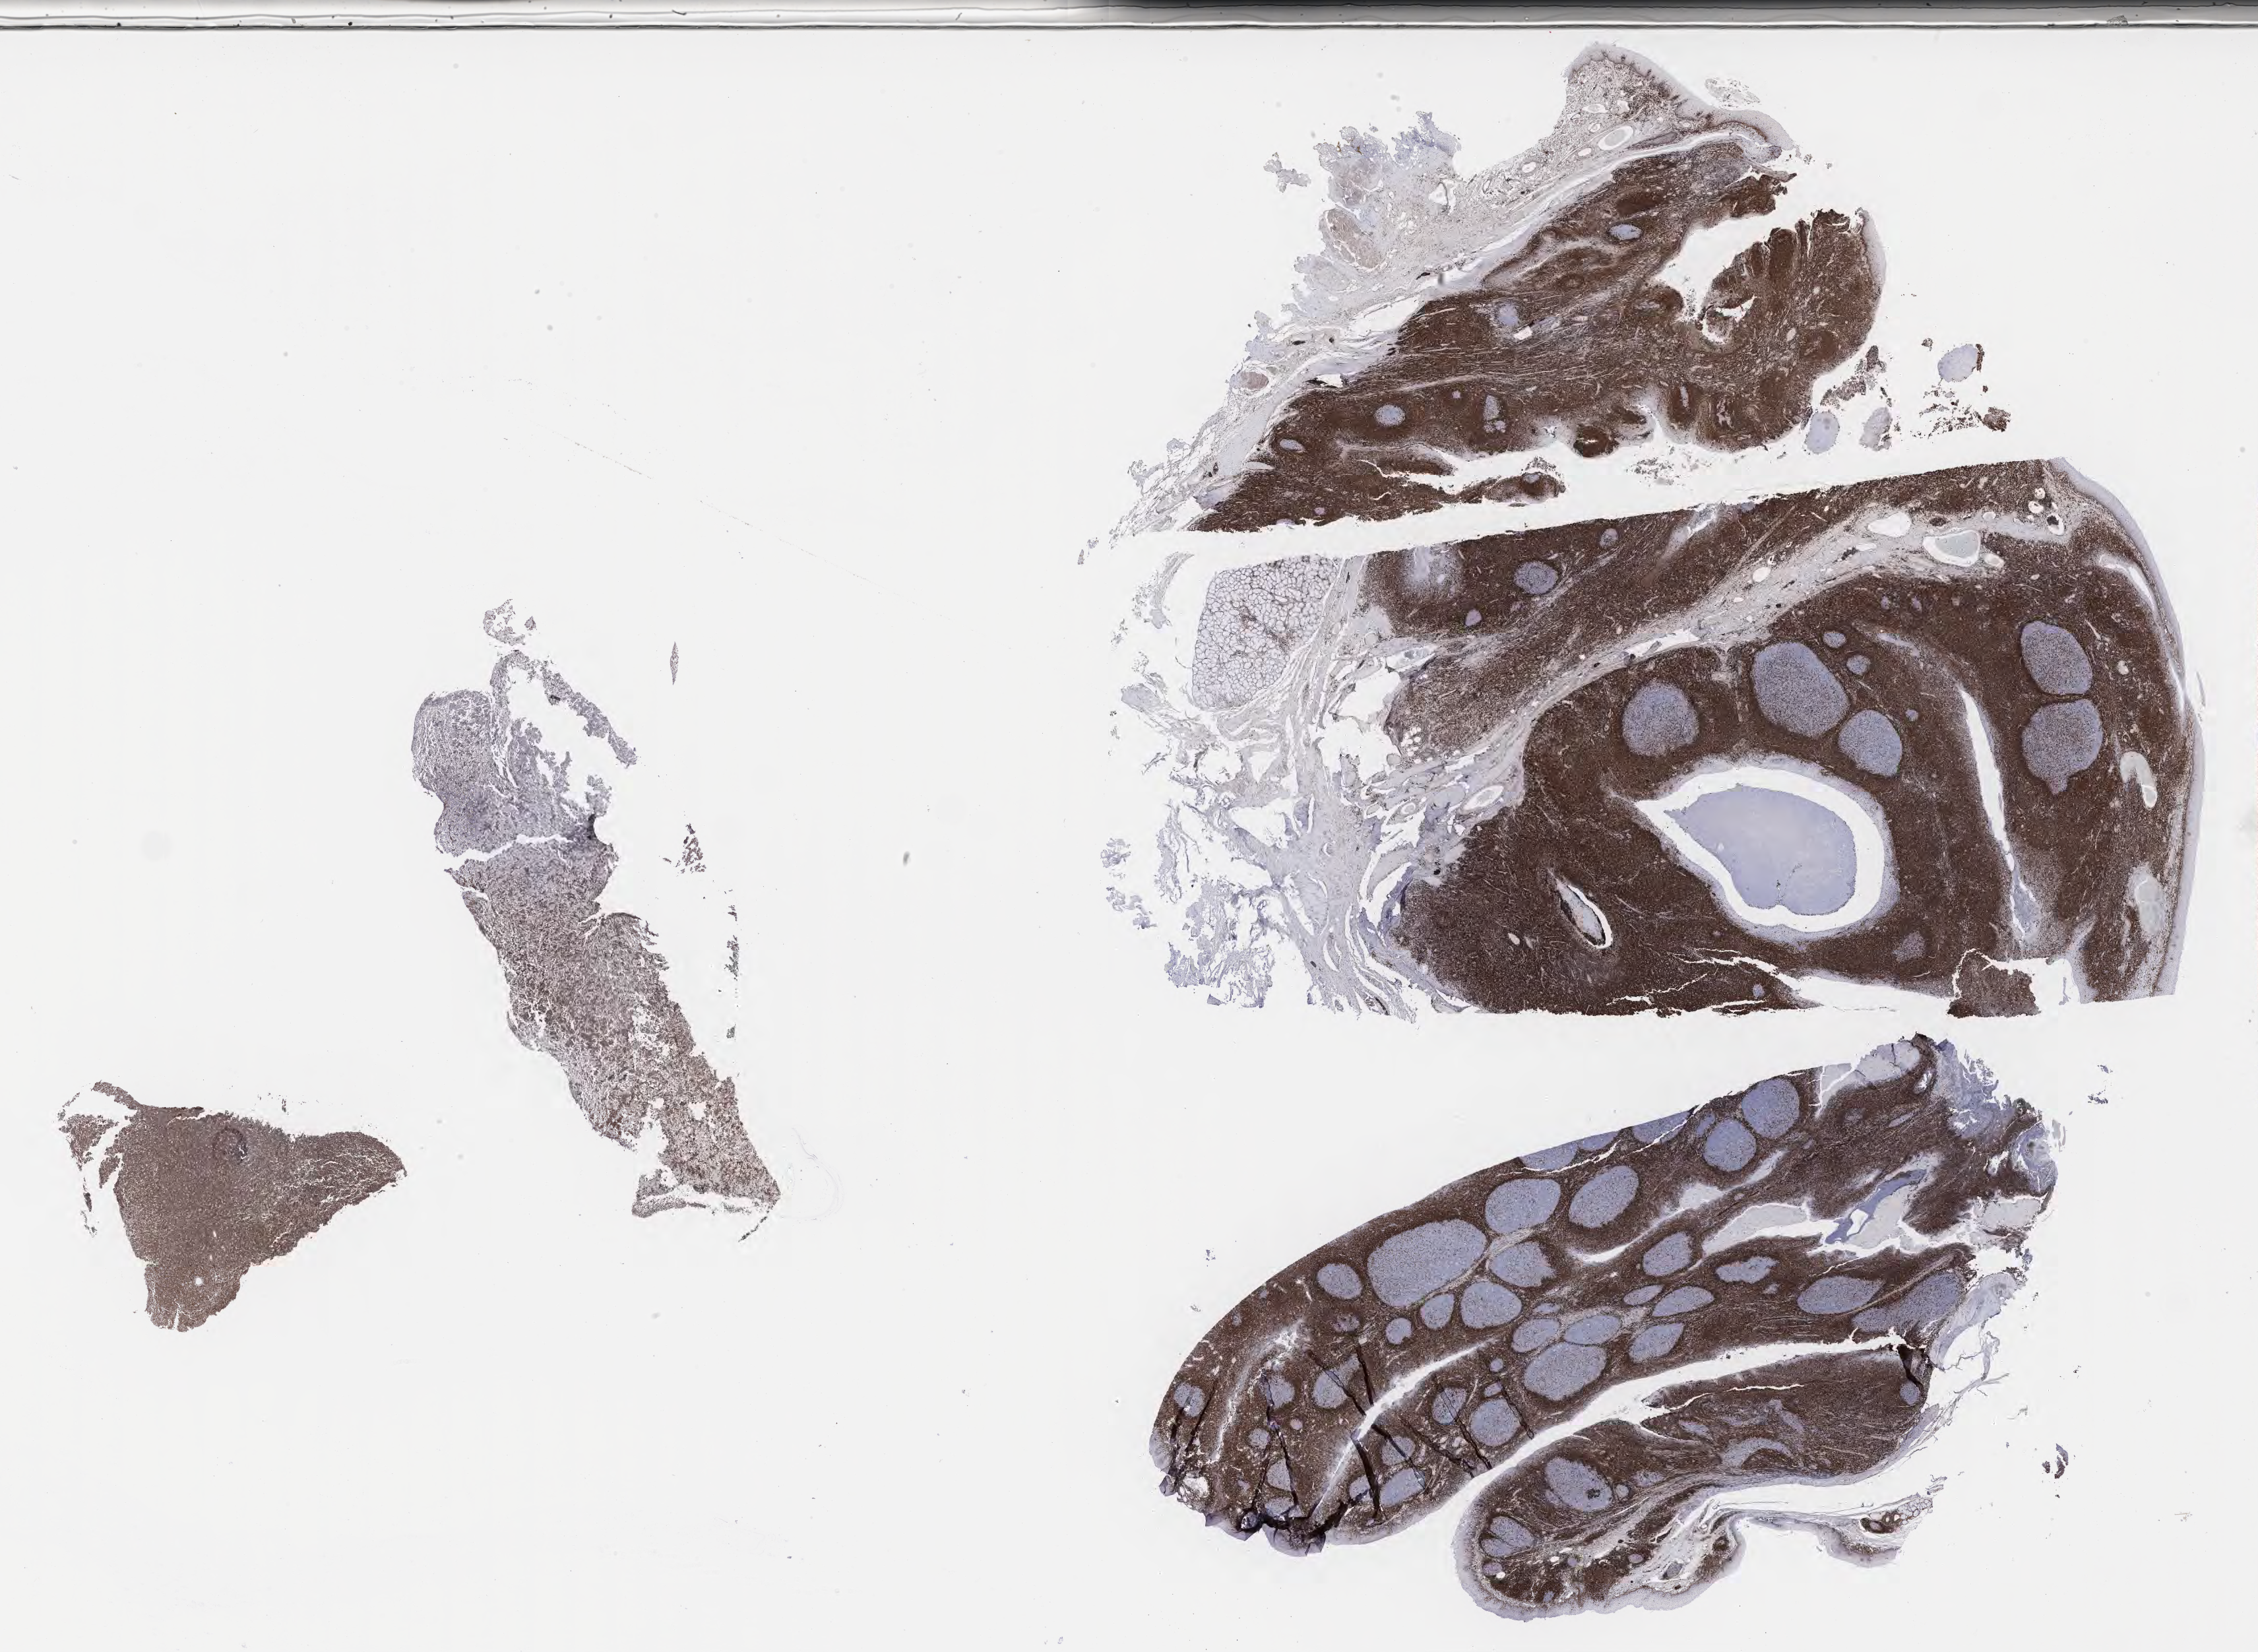
Immunohistochemistry (IHC) whole-slide image stained for BCL2, whole scanned area (about 27.7 x 20.2 mm) shown as a low-resolution overview; specimen: tumor tissue. Patient: male, age at initial diagnosis 2 years.
* histologic diagnosis: Burkitt lymphoma, NOS